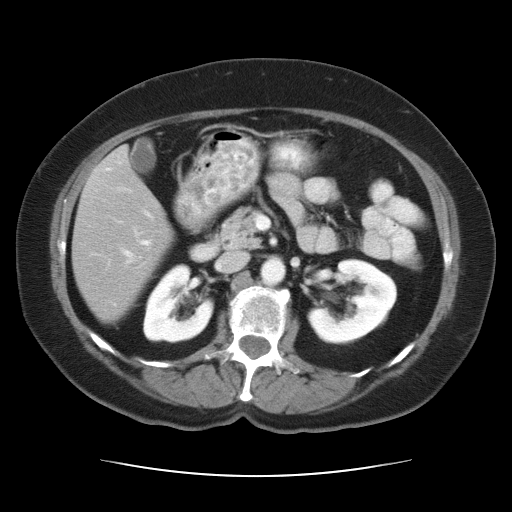
Contrast-enhanced abdominal CT, one axial slice. Position 14 of 34 along the scan axis. Reconstruction kernel STANDARD. 120 kVp. Intravenous contrast given. Soft-tissue window (W 400 / L 40 HU). 512 × 512 image matrix, field of view 360 × 360 mm. Female patient, age 65 years. From the clinical record (not read from this slice): diagnosis: colorectal cancer liver metastases, imaged before liver resection; multiple liver metastases: yes; largest metastasis: 2.2 cm; disease in both lobes: no.
Annotated regions visible in this slice (expert manual segmentation):
- hepatic veins: bounding box (x1, y1, x2, y2) in pixels: (118, 188, 246, 270)
- liver: (73, 150, 170, 317)
- planned liver remnant (the part of the liver to remain after resection): (73, 149, 170, 317)
- portal vein (with intrahepatic branches): (141, 211, 152, 245)